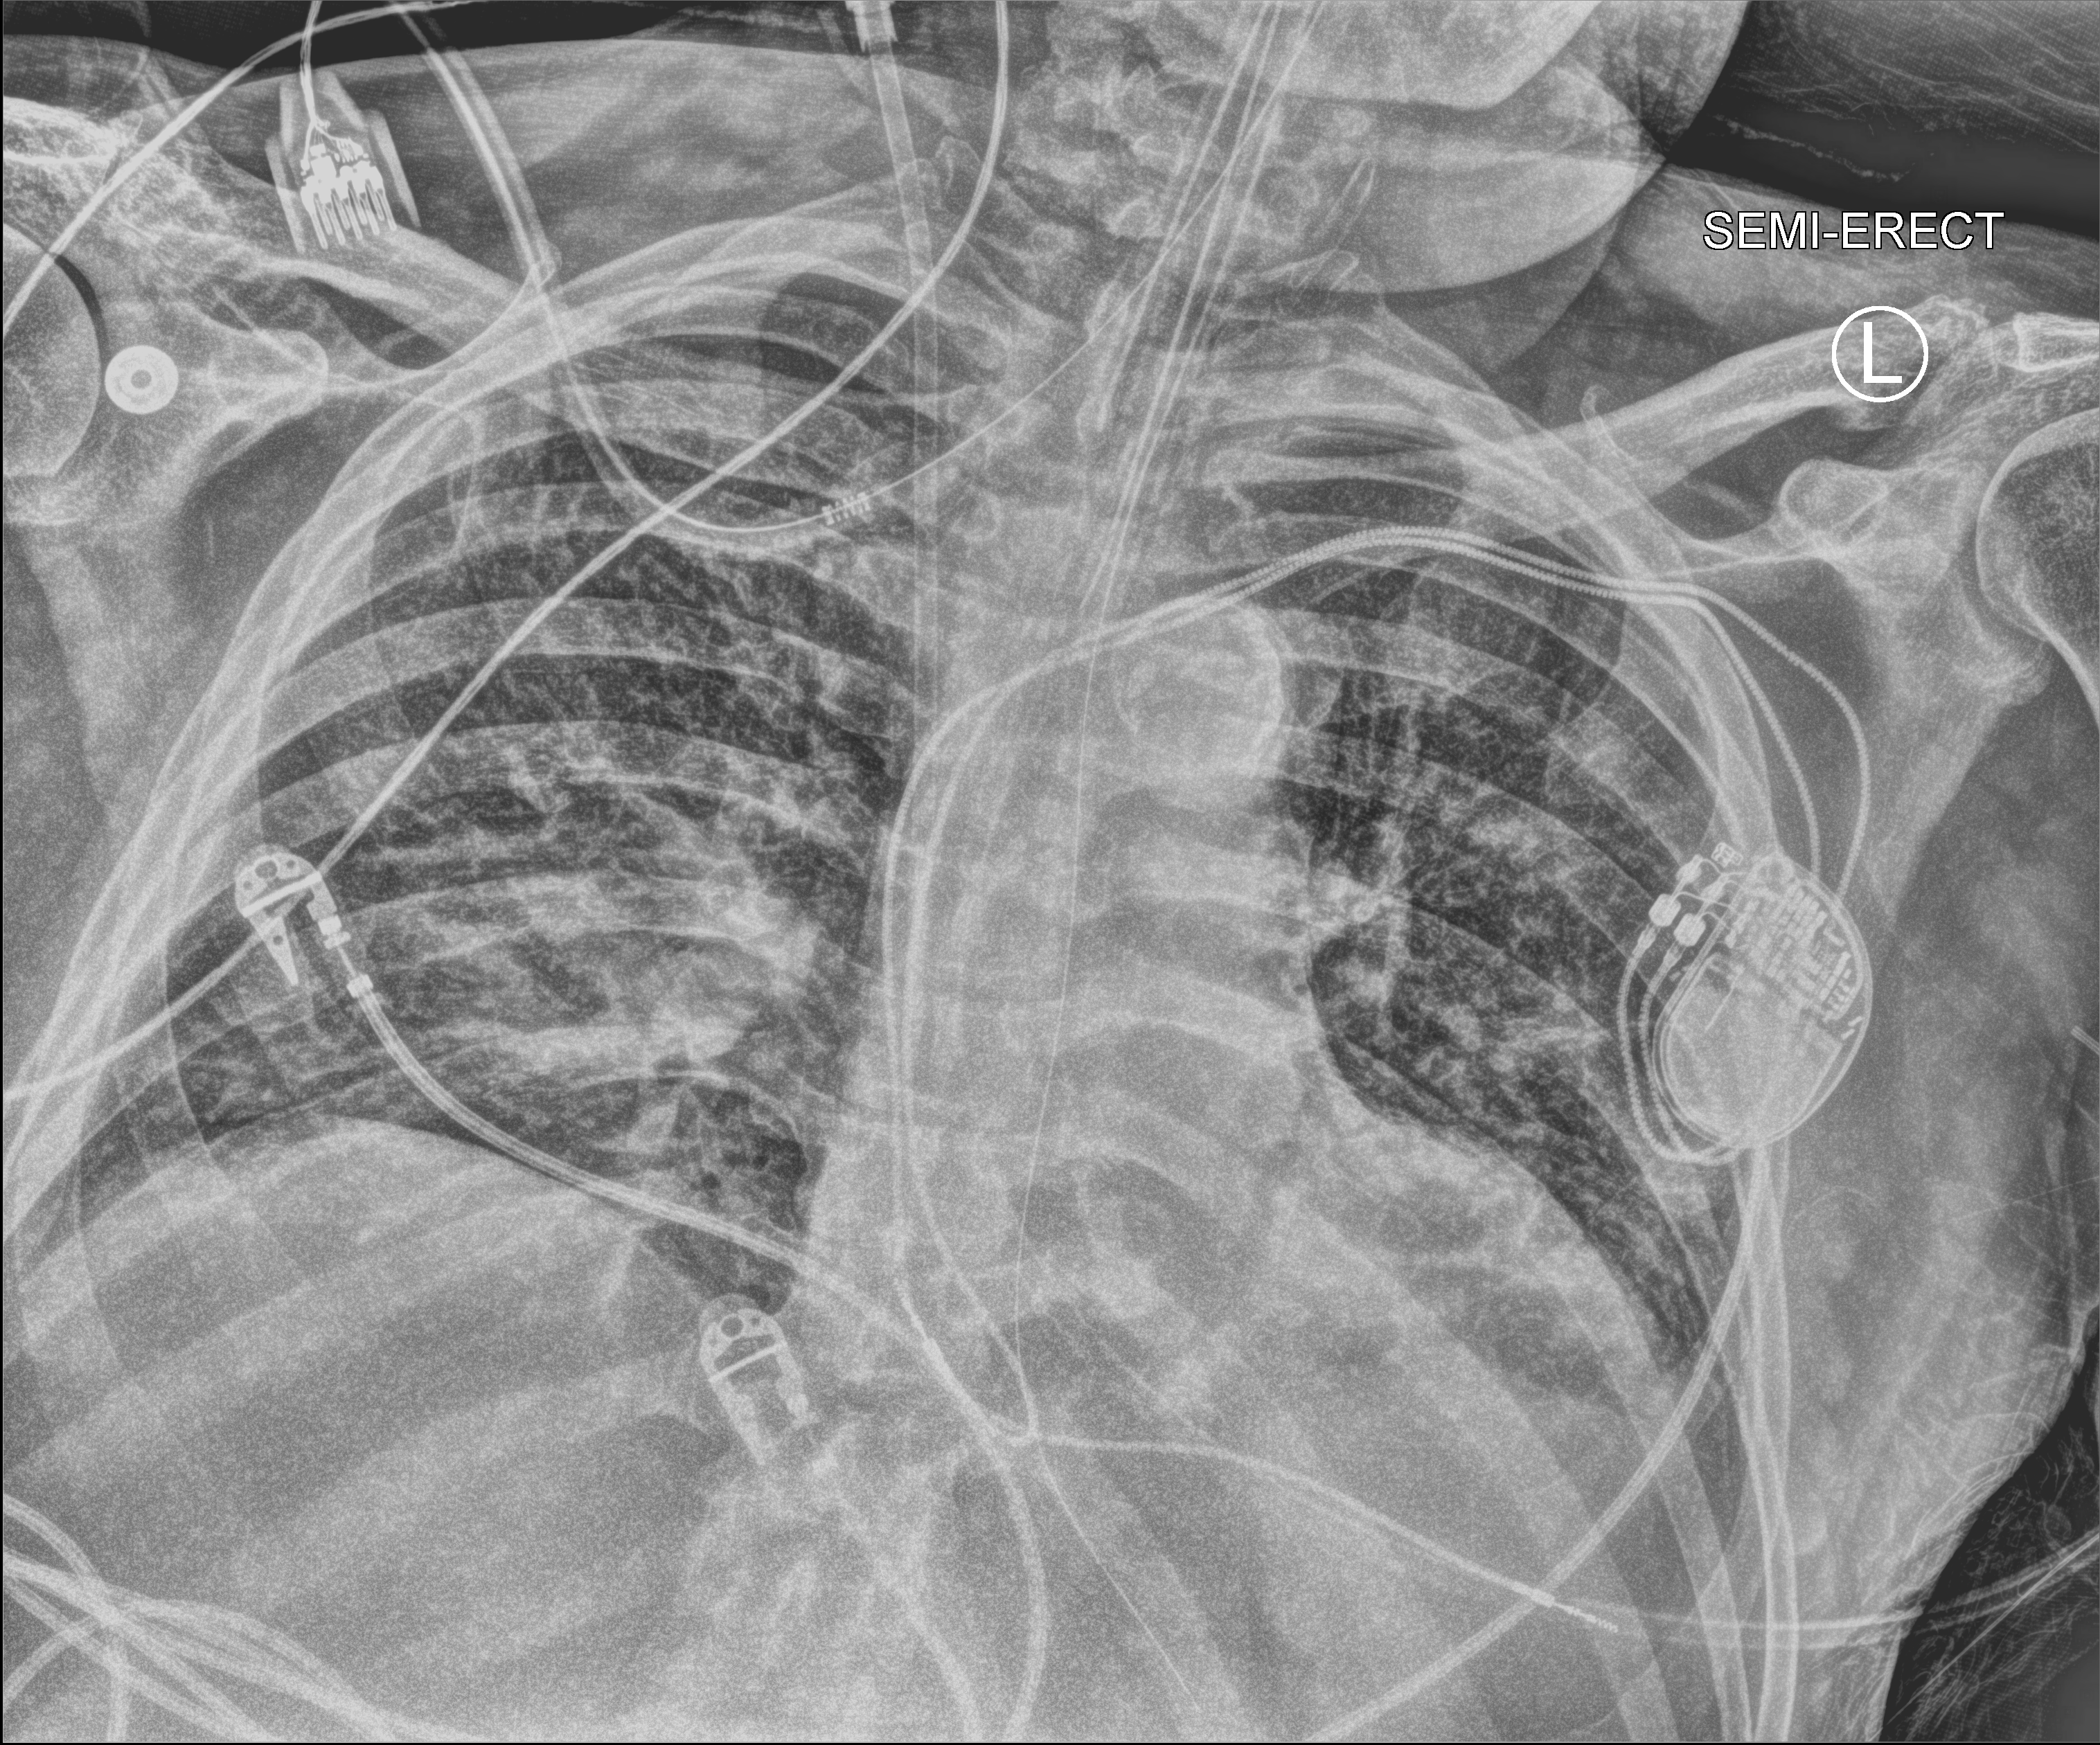
Portable chest radiograph, anteroposterior (AP) projection. Male patient hospitalised with COVID-19, age 60–74 years.
Hospital-stay facts (about this admission, not read from this image; timing relative to this image not recorded):
- admitted to intensive care during this hospital stay: yes
- mechanically ventilated during this hospital stay: yes